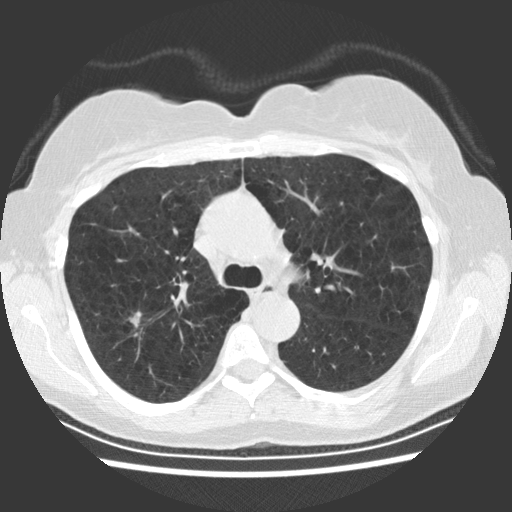
Low-dose screening chest CT, one axial slice; slice 160 of 234 in the series (ordered by position); reconstruction kernel STANDARD; lung window (W 1500 / L -600 HU); 2.5 mm slice thickness; 512 × 512 image matrix, field of view 330 × 330 mm.
Outlined on this slice (expert manual segmentation):
- lesion 1 (tumor, upper lobe of right lung): box from (x=130, y=315) to (x=140, y=327) px